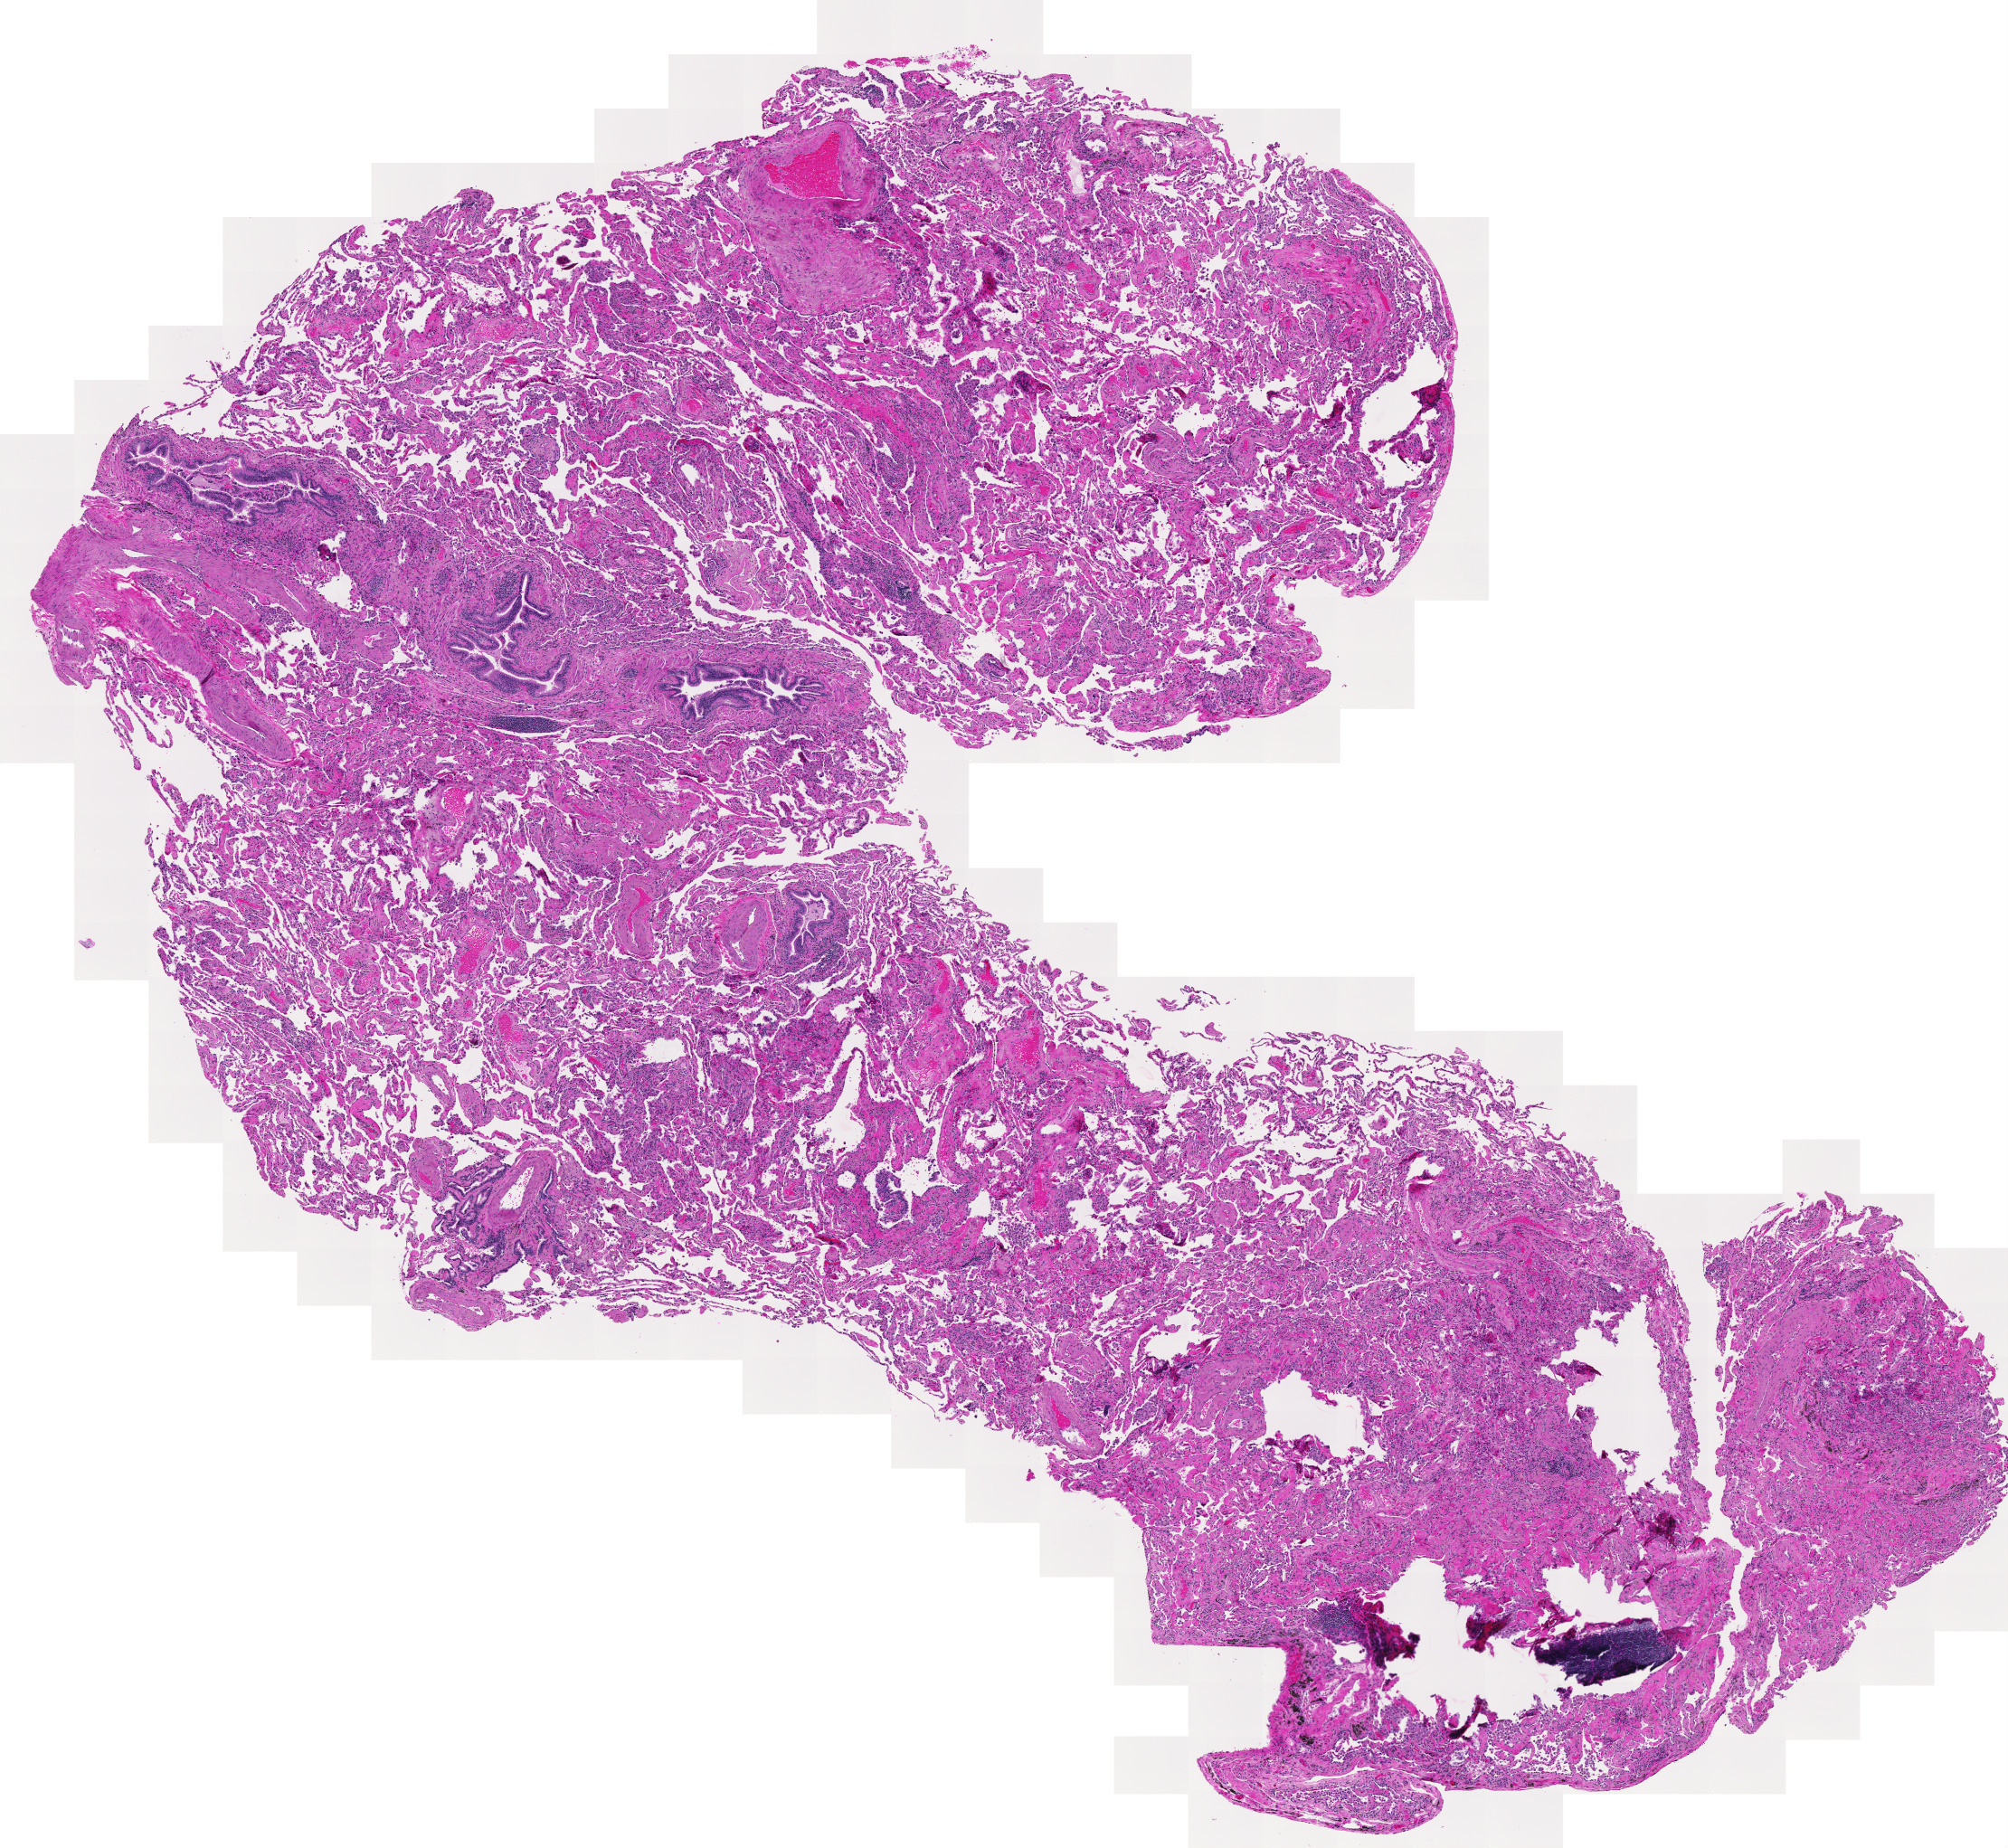
Hematoxylin and eosin (H&E) stained whole-slide image, a low-resolution overview of the entire scanned area, about 11.5 x 10.6 mm, normal (non-tumour) tissue sample, sampled site: lung. Male, 64 y/o.
- this section: normal (non-tumour) tissue from the same patient
- patient diagnosis: Adenocarcinoma, NOS